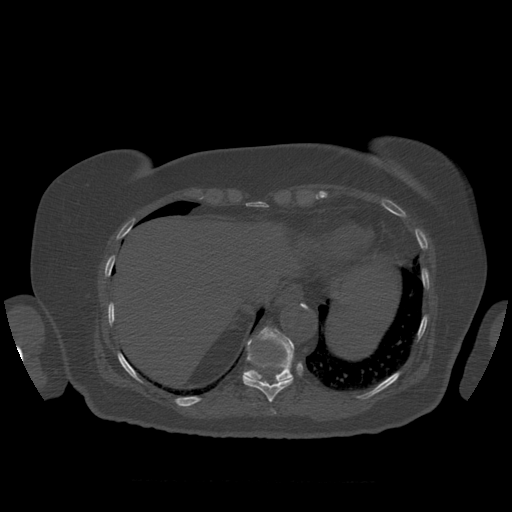
CT including the spine, one axial slice. Position 334 of 399 along the scan axis. Reconstruction kernel STANDARD. Bone window (W 1800 / L 400 HU). 1.25 mm slice thickness. 512 × 512 image matrix. Patient age 81 years. From the clinical record (not read from this slice): primary cancer: renal; vertebrae with lytic lesions (as recorded): L1.
Structures marked on this image (semi-automatically segmented with operator editing):
- T10 vertebra: bounding box <243,354,294,402> (left, top, right, bottom; pixels)
- T11 vertebra: <243,327,295,382>
- T9 vertebra: <273,410,276,414>